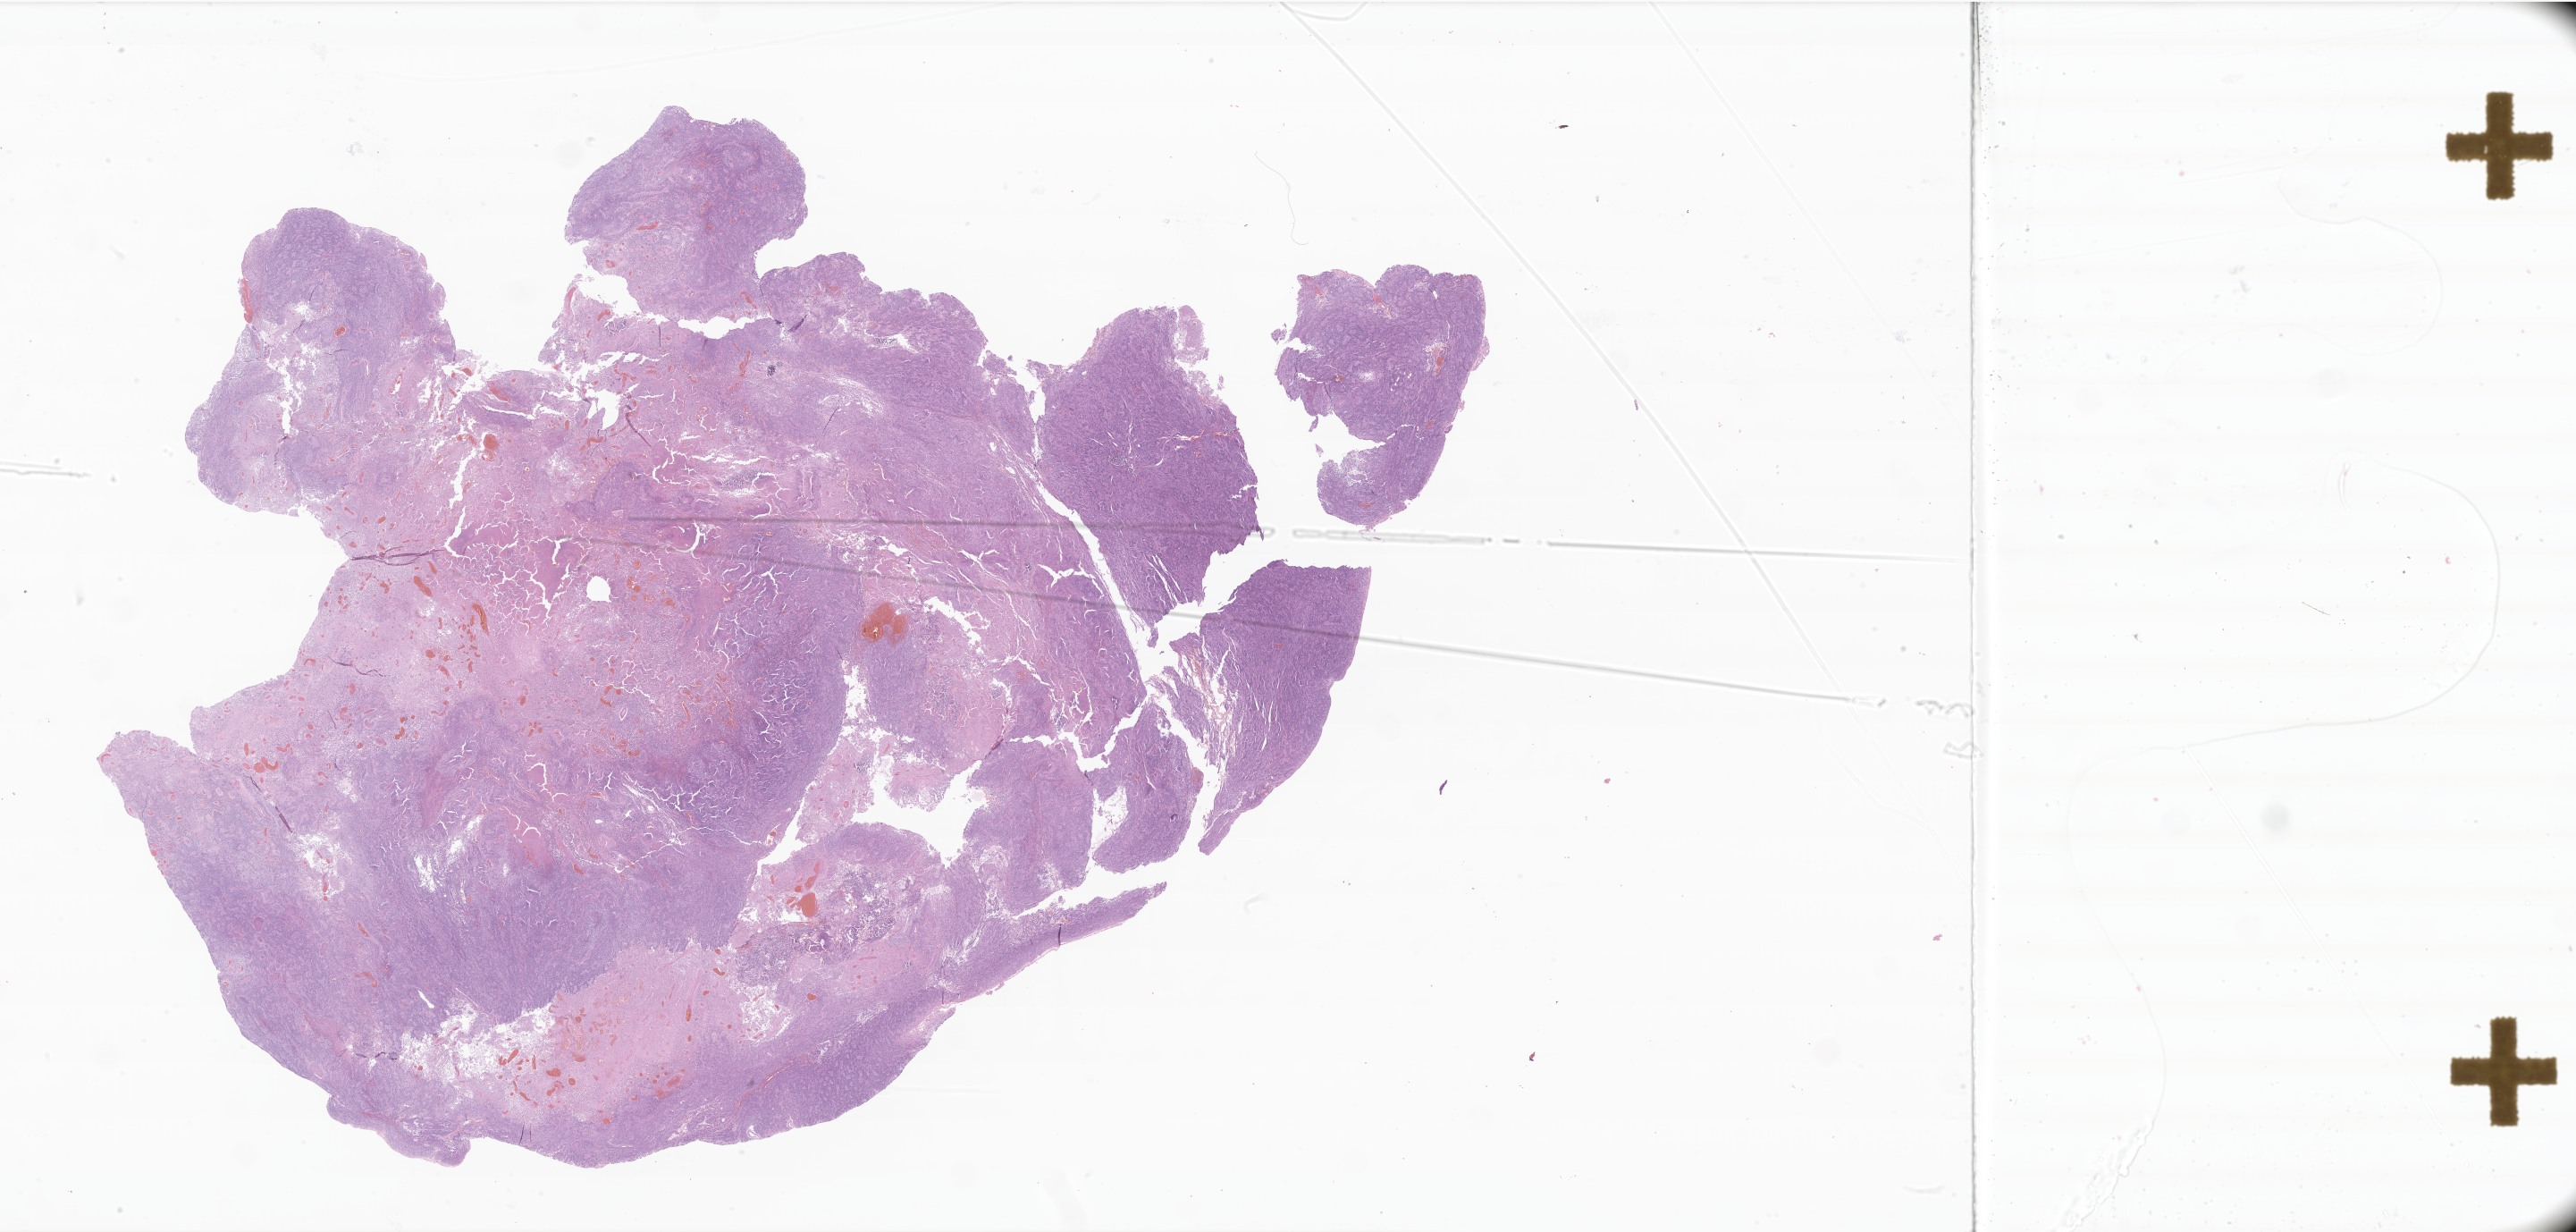
Digitized haematoxylin and eosin-stained section of tumor tissue from the brain, low-resolution overview of the scanned area, about 48.6 x 23.2 mm, FFPE section. Patient: male, age 47 months (3 years 11 months).
Recorded diagnosis: Ependymoma, anaplastic.